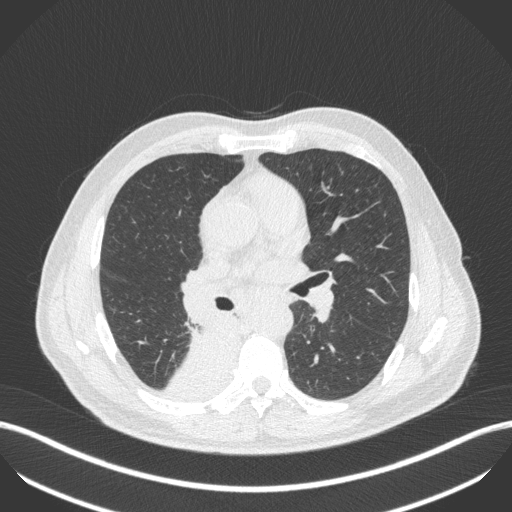
Chest CT, one axial slice; 100 kVp; lung window (W 1500 / L -600 HU); 1 mm slice thickness; 512 × 512 image matrix, field of view 400 × 400 mm. Male patient, age 61 years. From the clinical record (not read from this slice): clinical TNM (as recorded): T1 N0 M0; histopathological grade: G3.
Annotated regions visible in this slice (rectangle marked by the reading radiologist):
- lung tumour (recorded histology: small cell carcinoma): bounding box <156,318,241,399> (left, top, right, bottom; pixels)